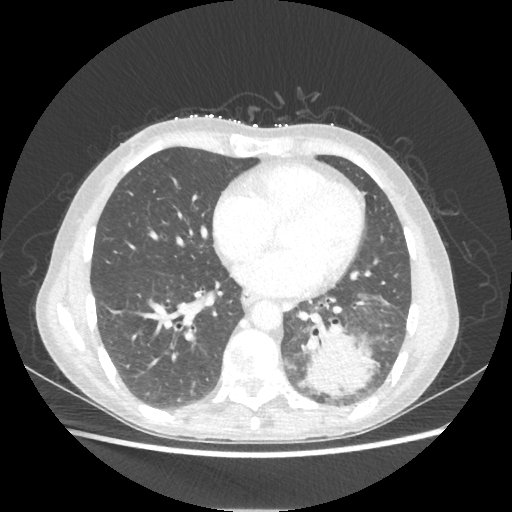
Chest CT, one axial slice; slice 90 of 221 in the series (ordered by position); reconstruction kernel STANDARD; lung window (W 1500 / L -600 HU); 1.25 mm slice thickness; 512 × 512 image matrix, field of view 360 × 360 mm. Patient: female, 53 years. Case-level facts recorded for this patient, not image findings: clinical TNM (as recorded): T3 N0 M0.
Structures marked on this image (bounding box drawn by a radiologist):
- lung tumour (recorded histology: adenocarcinoma): box from (x=304, y=322) to (x=374, y=395) px